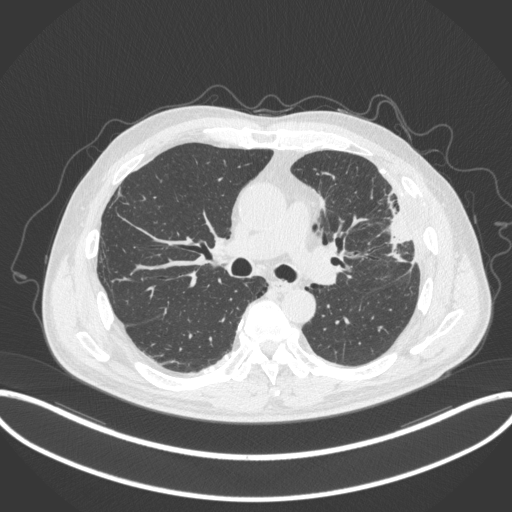
Chest CT, one axial slice. Position 203 of 382 along the scan axis. Reconstruction kernel B31f. 120 kVp. Lung window (W 1500 / L -600 HU). 1 mm slice thickness. 512 × 512 image matrix, field of view 415 × 415 mm. Male patient, age 64 years. From the clinical record (not read from this slice): clinical TNM (as recorded): T4 N1 M0; histopathological grade: G3.
Annotated regions visible in this slice (rectangle marked by the reading radiologist):
- lung tumour (recorded histology: adenocarcinoma): bounding box <377,189,415,268> (left, top, right, bottom; pixels)